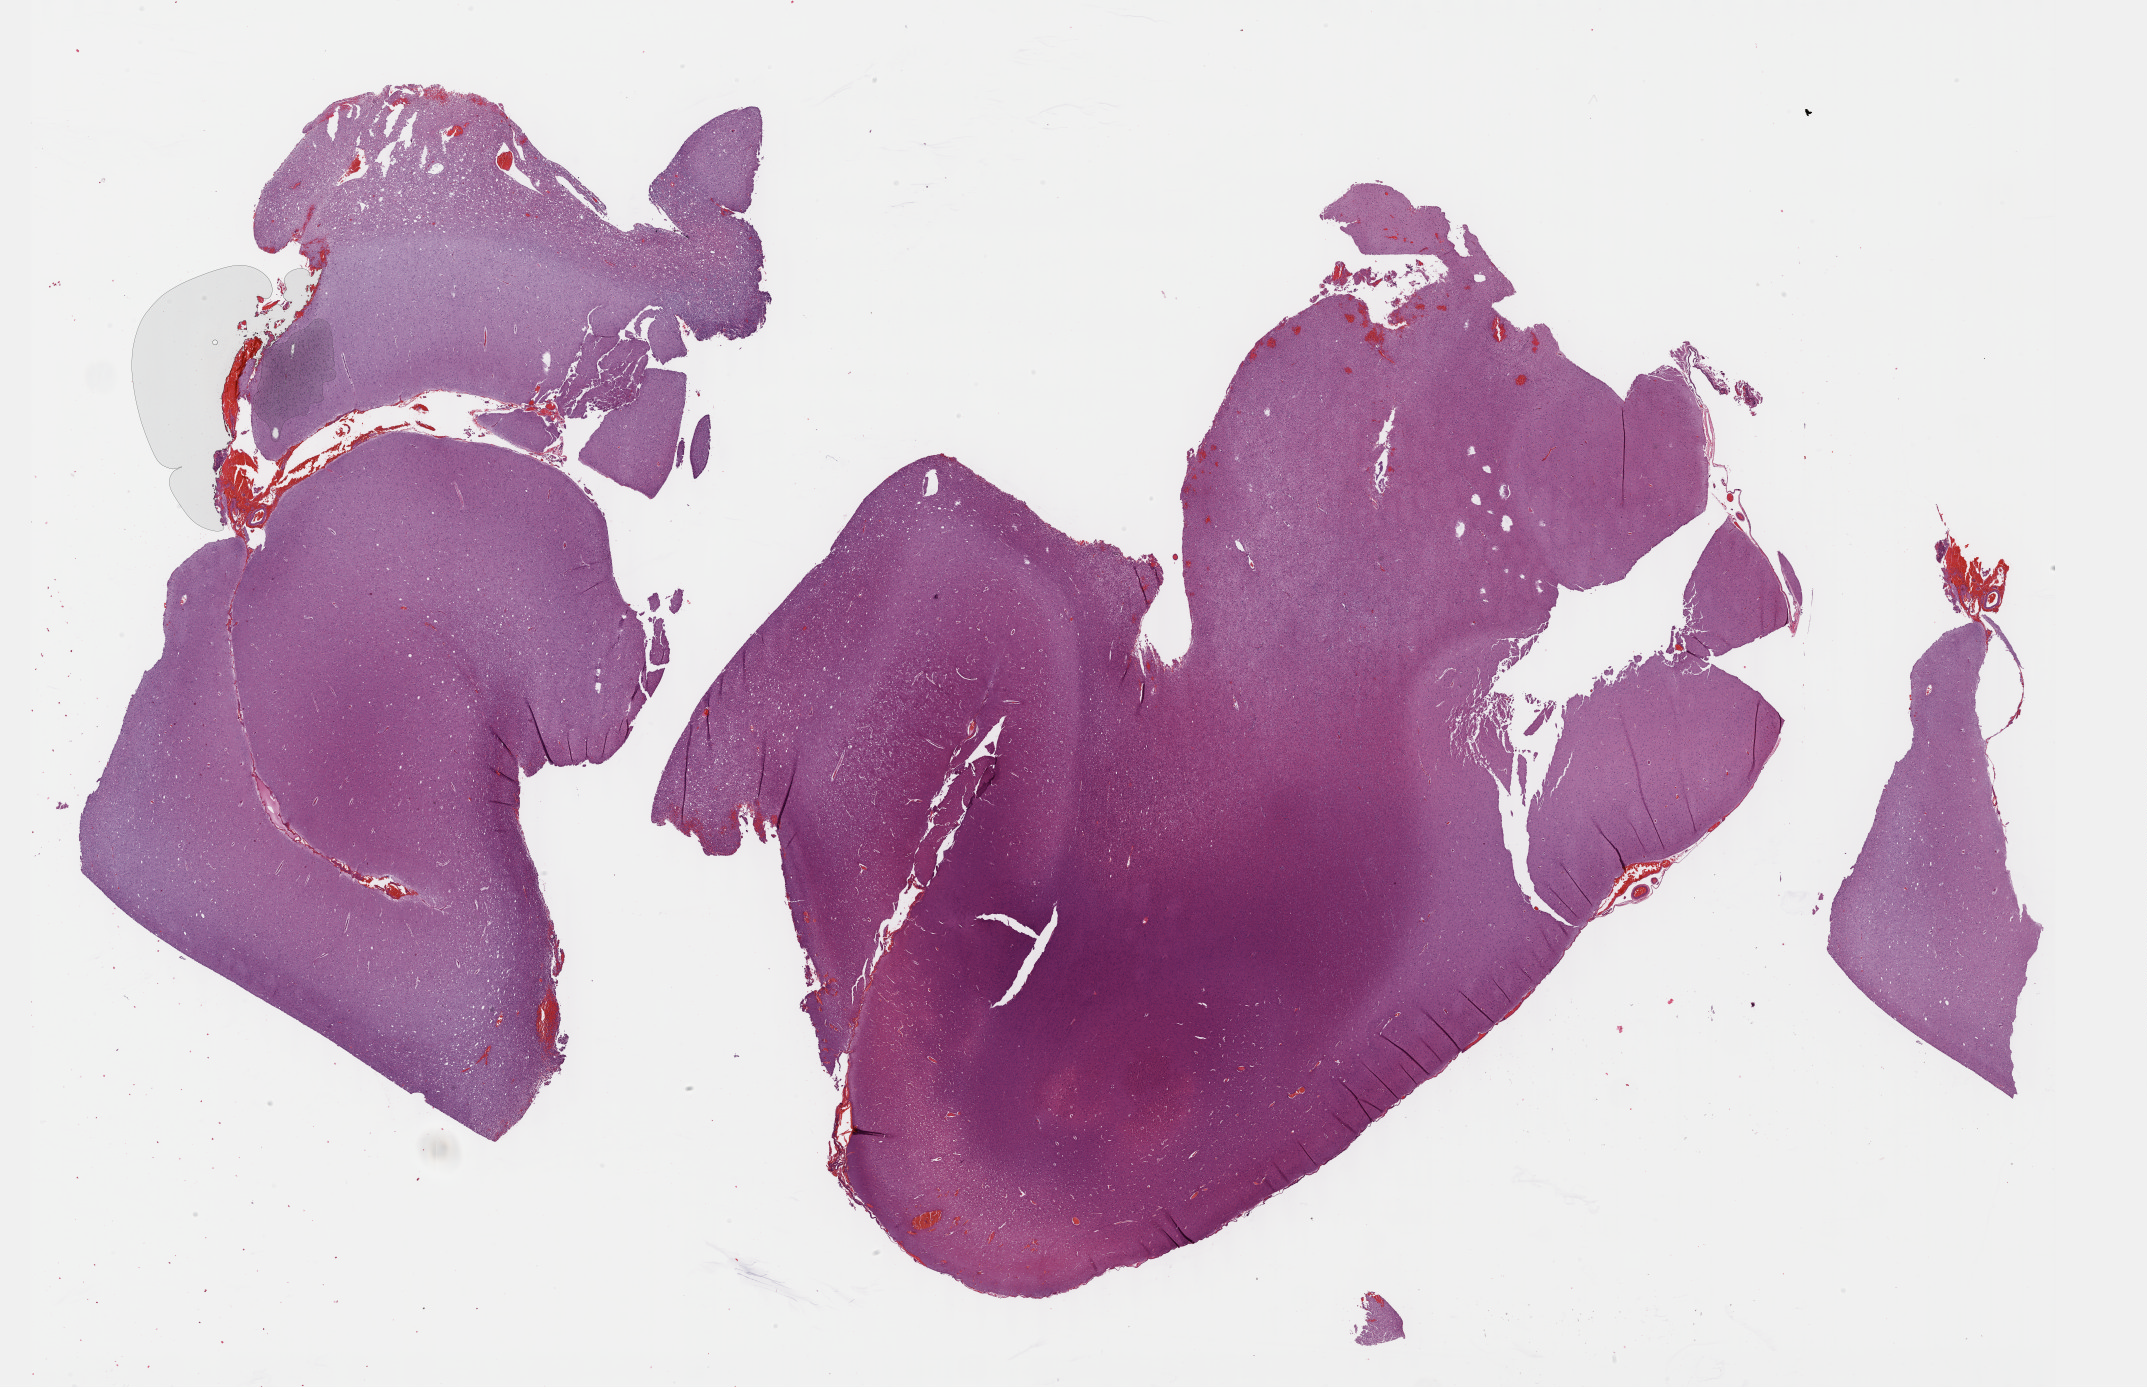
Digitized H&E tissue section (whole slide), a low-resolution overview of the entire scanned area, about 34.7 x 22.4 mm (acquisition: 40x scan), FFPE section, brain, primary tumour sample. Male patient; age at initial diagnosis 35 years. Histologic grade: G3 (poorly differentiated).
- laterality: left
- diagnosis: Oligodendroglioma, anaplastic (cerebrum)